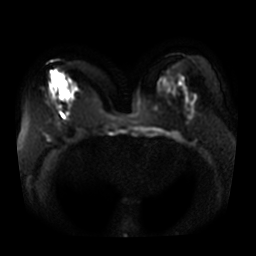
Breast MRI, one axial slice; position 17 of 36 along the scan axis; diffusion-weighted series; image 2 of 4 stored at this slice position (different b-values; order by instance number); 3 T; 5 mm slice thickness; 256 × 256 image matrix, field of view 370 × 370 mm. Female patient.
Outlined on this slice (outlined manually by an expert reader):
- tumour on diffusion-weighted imaging: bounding box <51,74,66,90> (left, top, right, bottom; pixels)